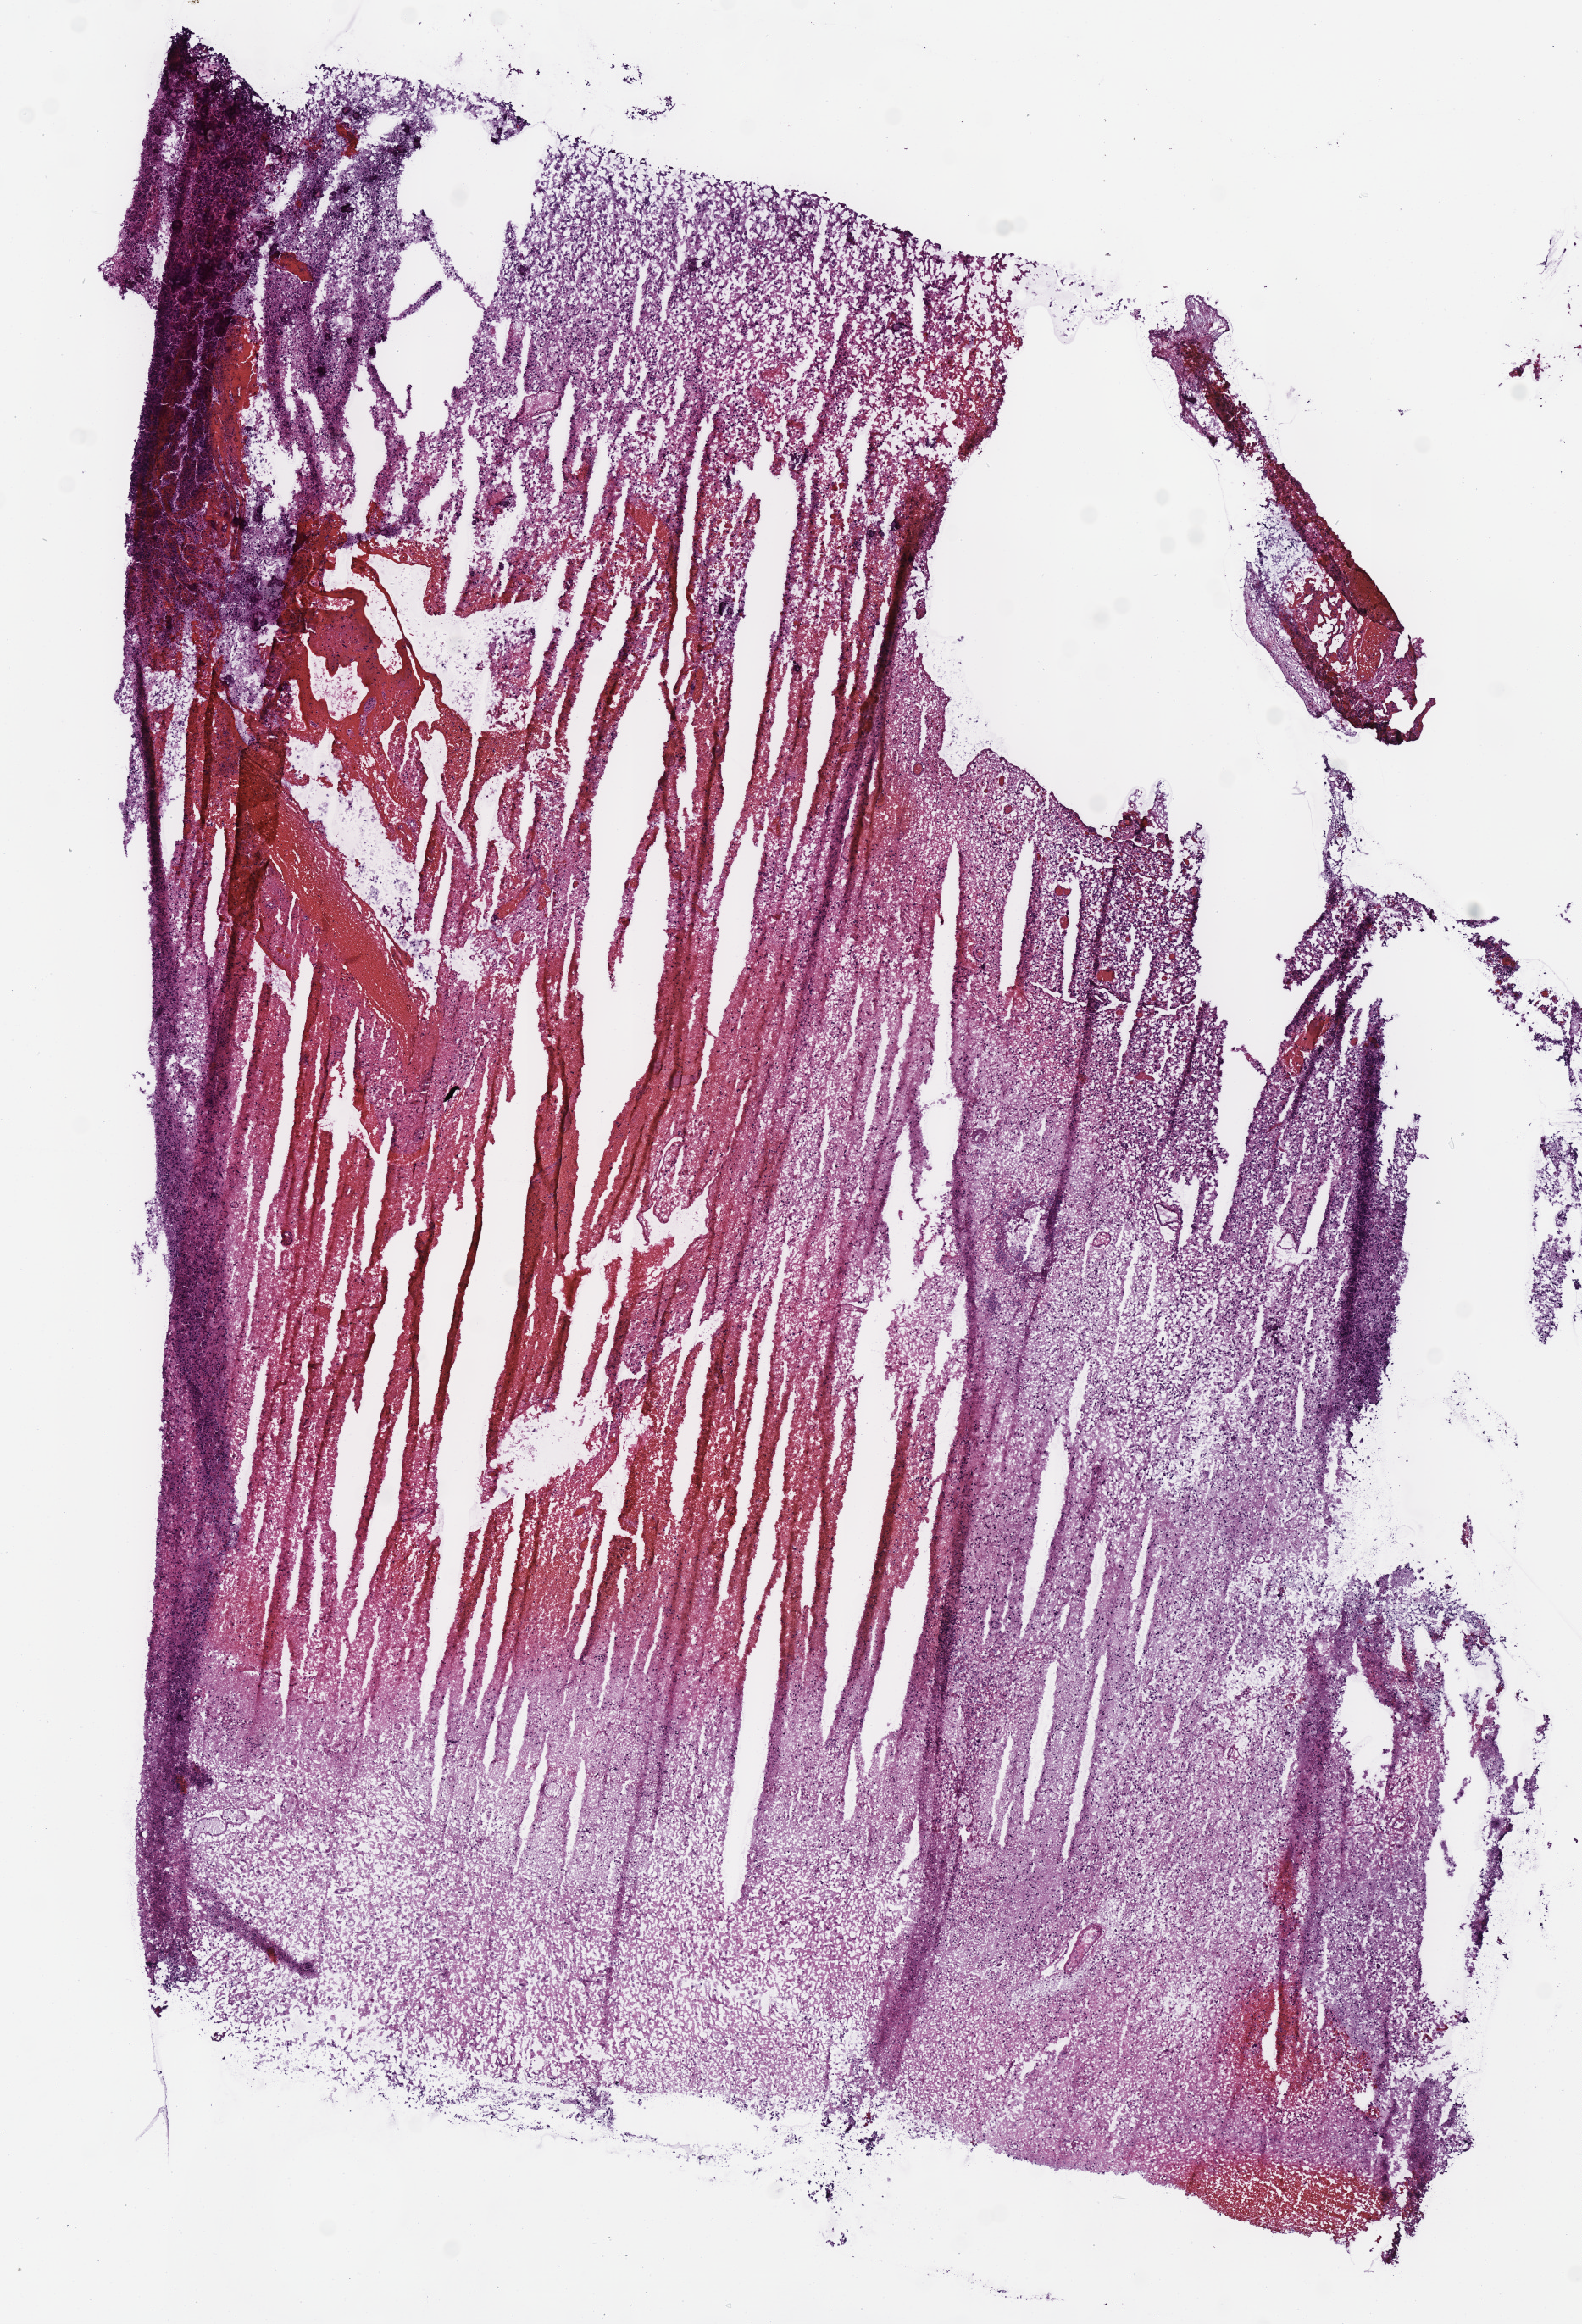
Whole-slide histology image, H&E — a low-resolution overview of the entire scanned area, about 7.3 x 10.8 mm (slide scanned at 40x); frozen section from the bottom of the tissue portion; primary tumour sample from the brain. Male, age 54 years at initial diagnosis. Histologic grade: G3 (poorly differentiated). Pathologist review of this section (percent, as recorded): tumour cells 100%, tumour nuclei 70%, normal cells 0%, stromal cells 0%, necrosis 0%.
Histologic diagnosis: Oligodendroglioma, anaplastic (cerebrum).